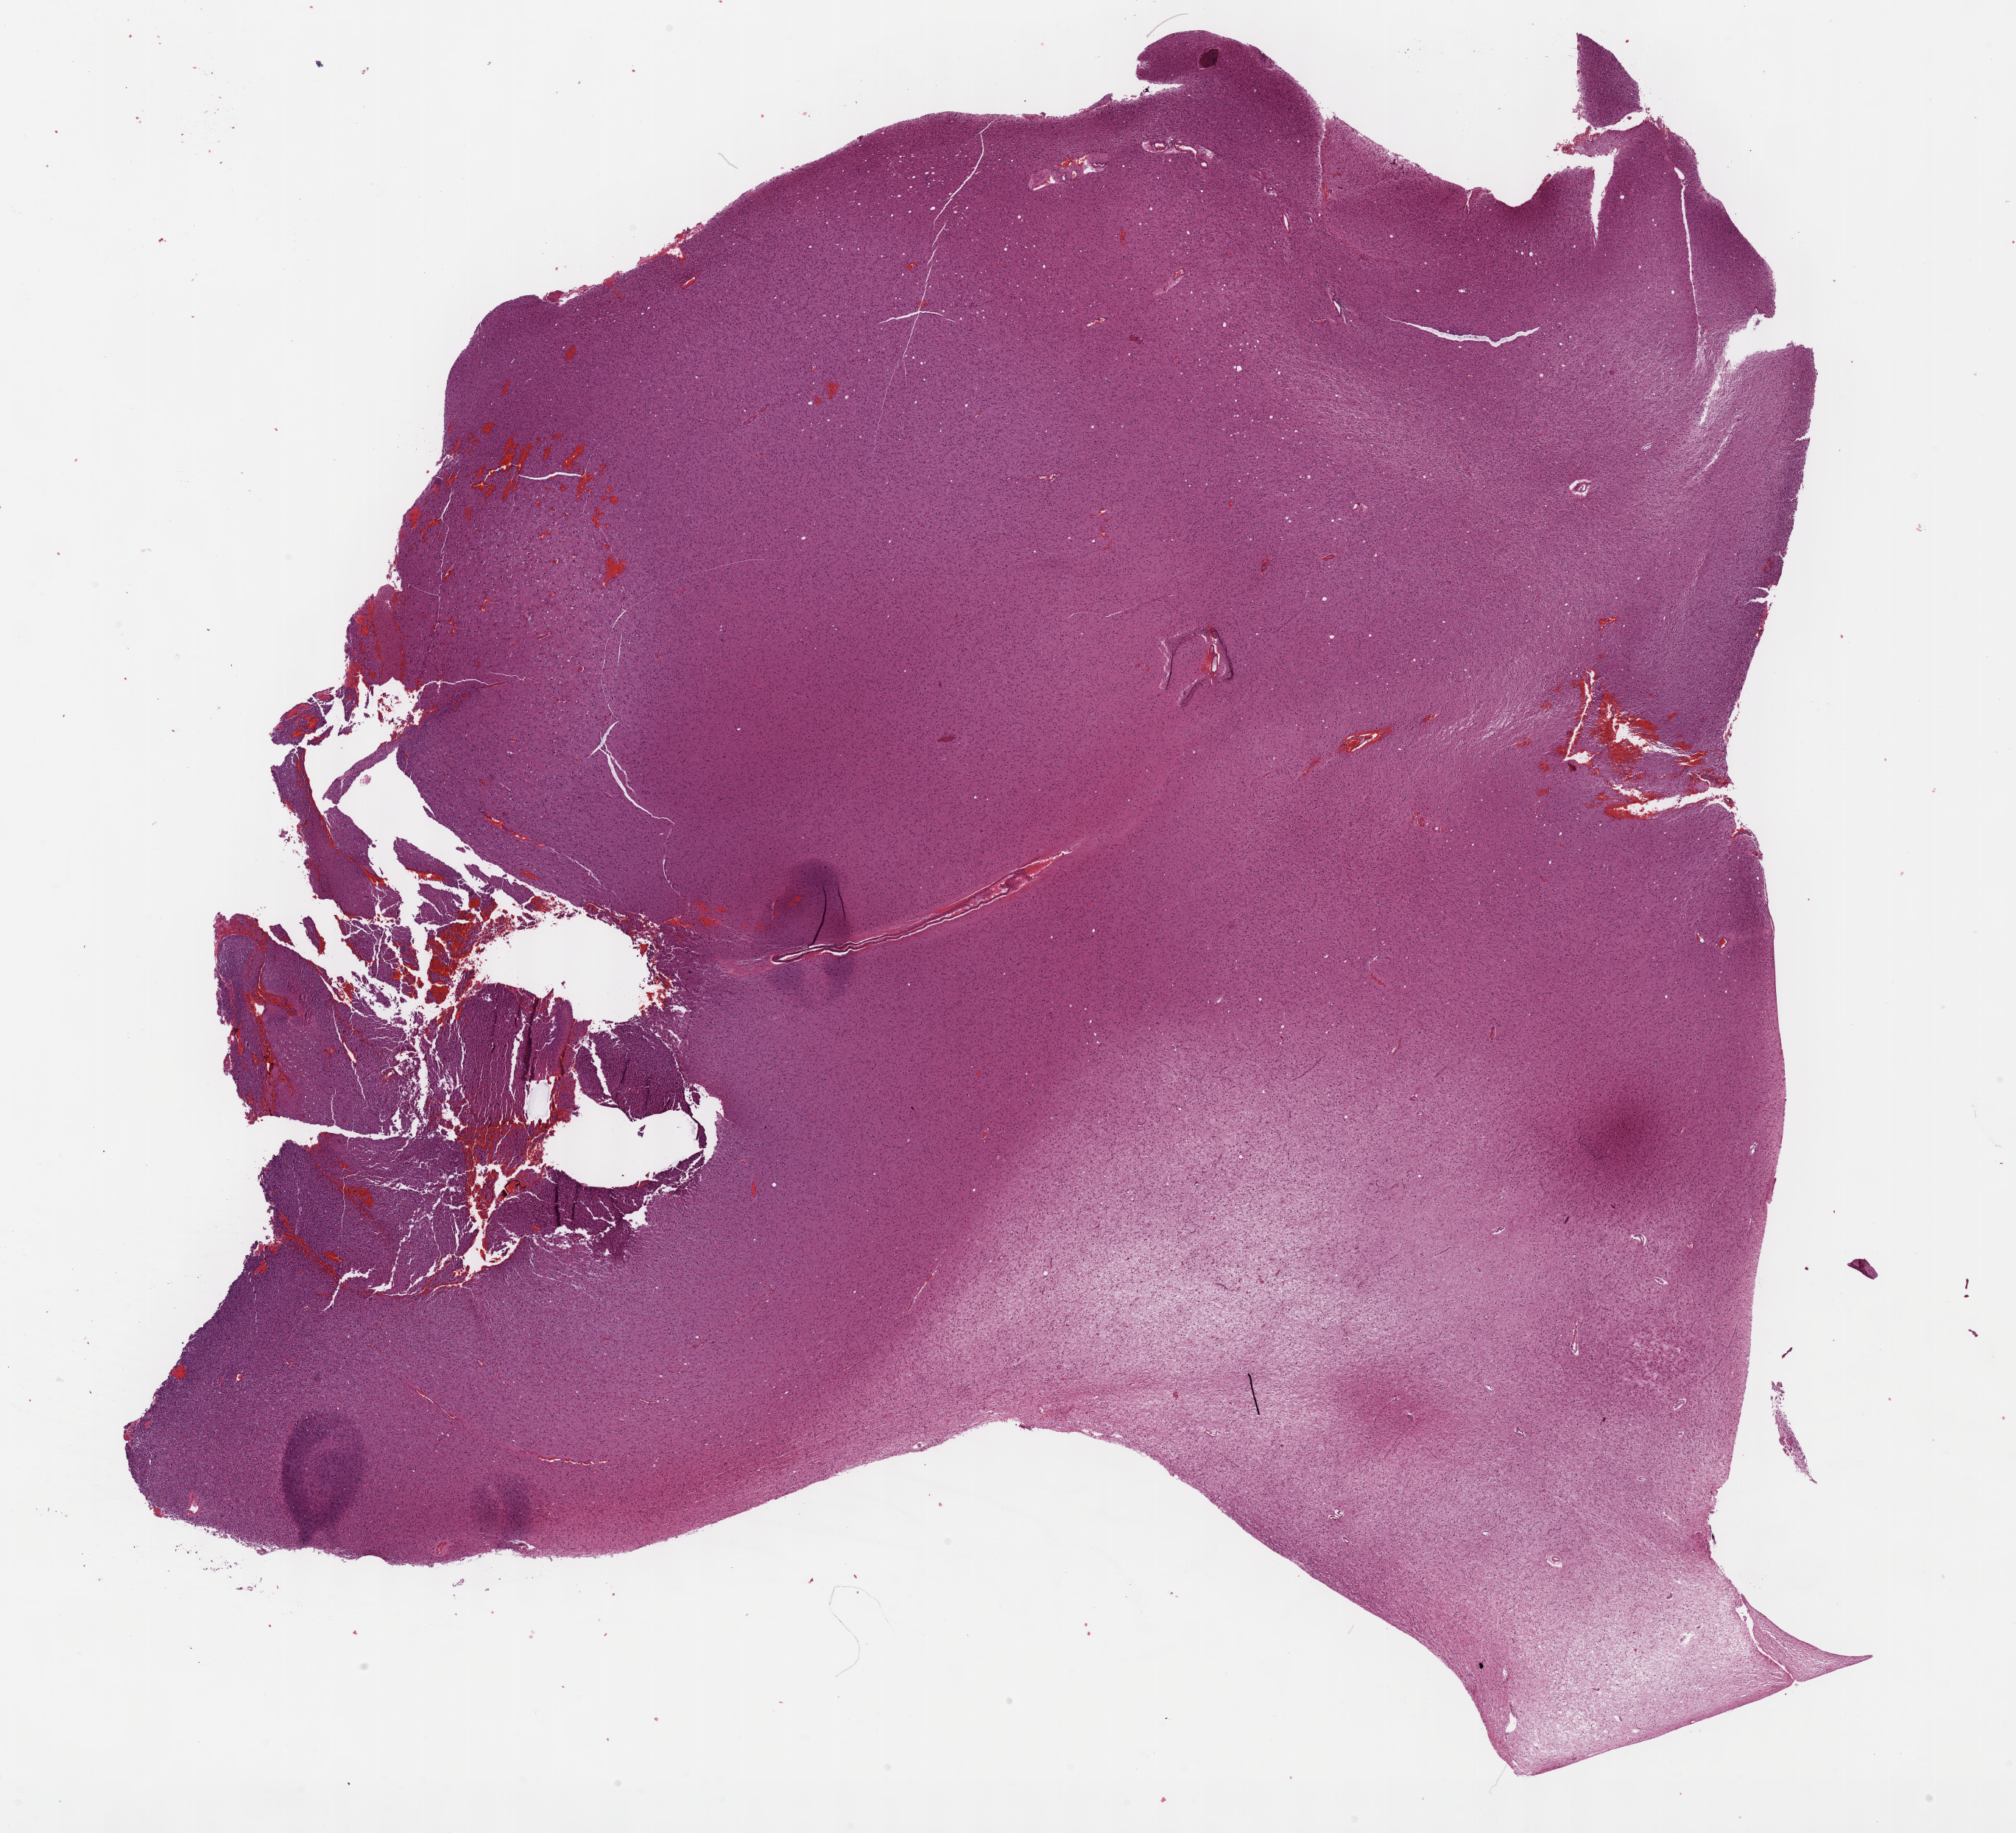
Hematoxylin and eosin (H&E) stained whole-slide image, a low-resolution overview of the entire scanned area, about 22.1 x 20.1 mm. FFPE section. Brain, primary tumour sample. Male, age 34 years at initial diagnosis. Histologic grade: G3 (poorly differentiated).
Diagnosis: Mixed glioma (cerebrum). Laterality: right.